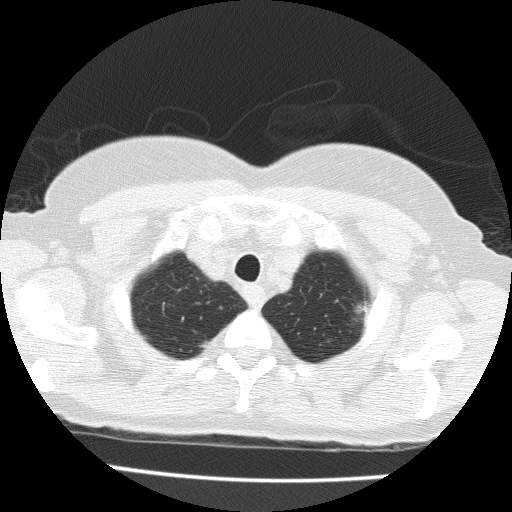
Axial slice from a low-dose chest CT screening exam. Baseline screening round. Lung window (W 1500 / L -600 HU). 2 mm slice thickness. 120 kVp. Slice 21 of 183 in the series. Female, age 71 years at enrolment. Former smoker at enrolment.
Expert reader's lesion annotation, bounding box (x1, y1, x2, y2) in pixels: (340, 292, 386, 333). The exam's reader record, not a measurement of the box and not confirmed to be the same lesion: non-calcified nodule or mass ≥4 mm, left upper lobe, 15 × 10 mm, spiculated (stellate) margins, soft tissue attenuation. Lung cancer was diagnosed 49 days after this screen: adenocarcinoma with mixed subtypes, left upper lobe, well differentiated (G1), stage IA (AJCC 6th edition), 15 mm at pathology.